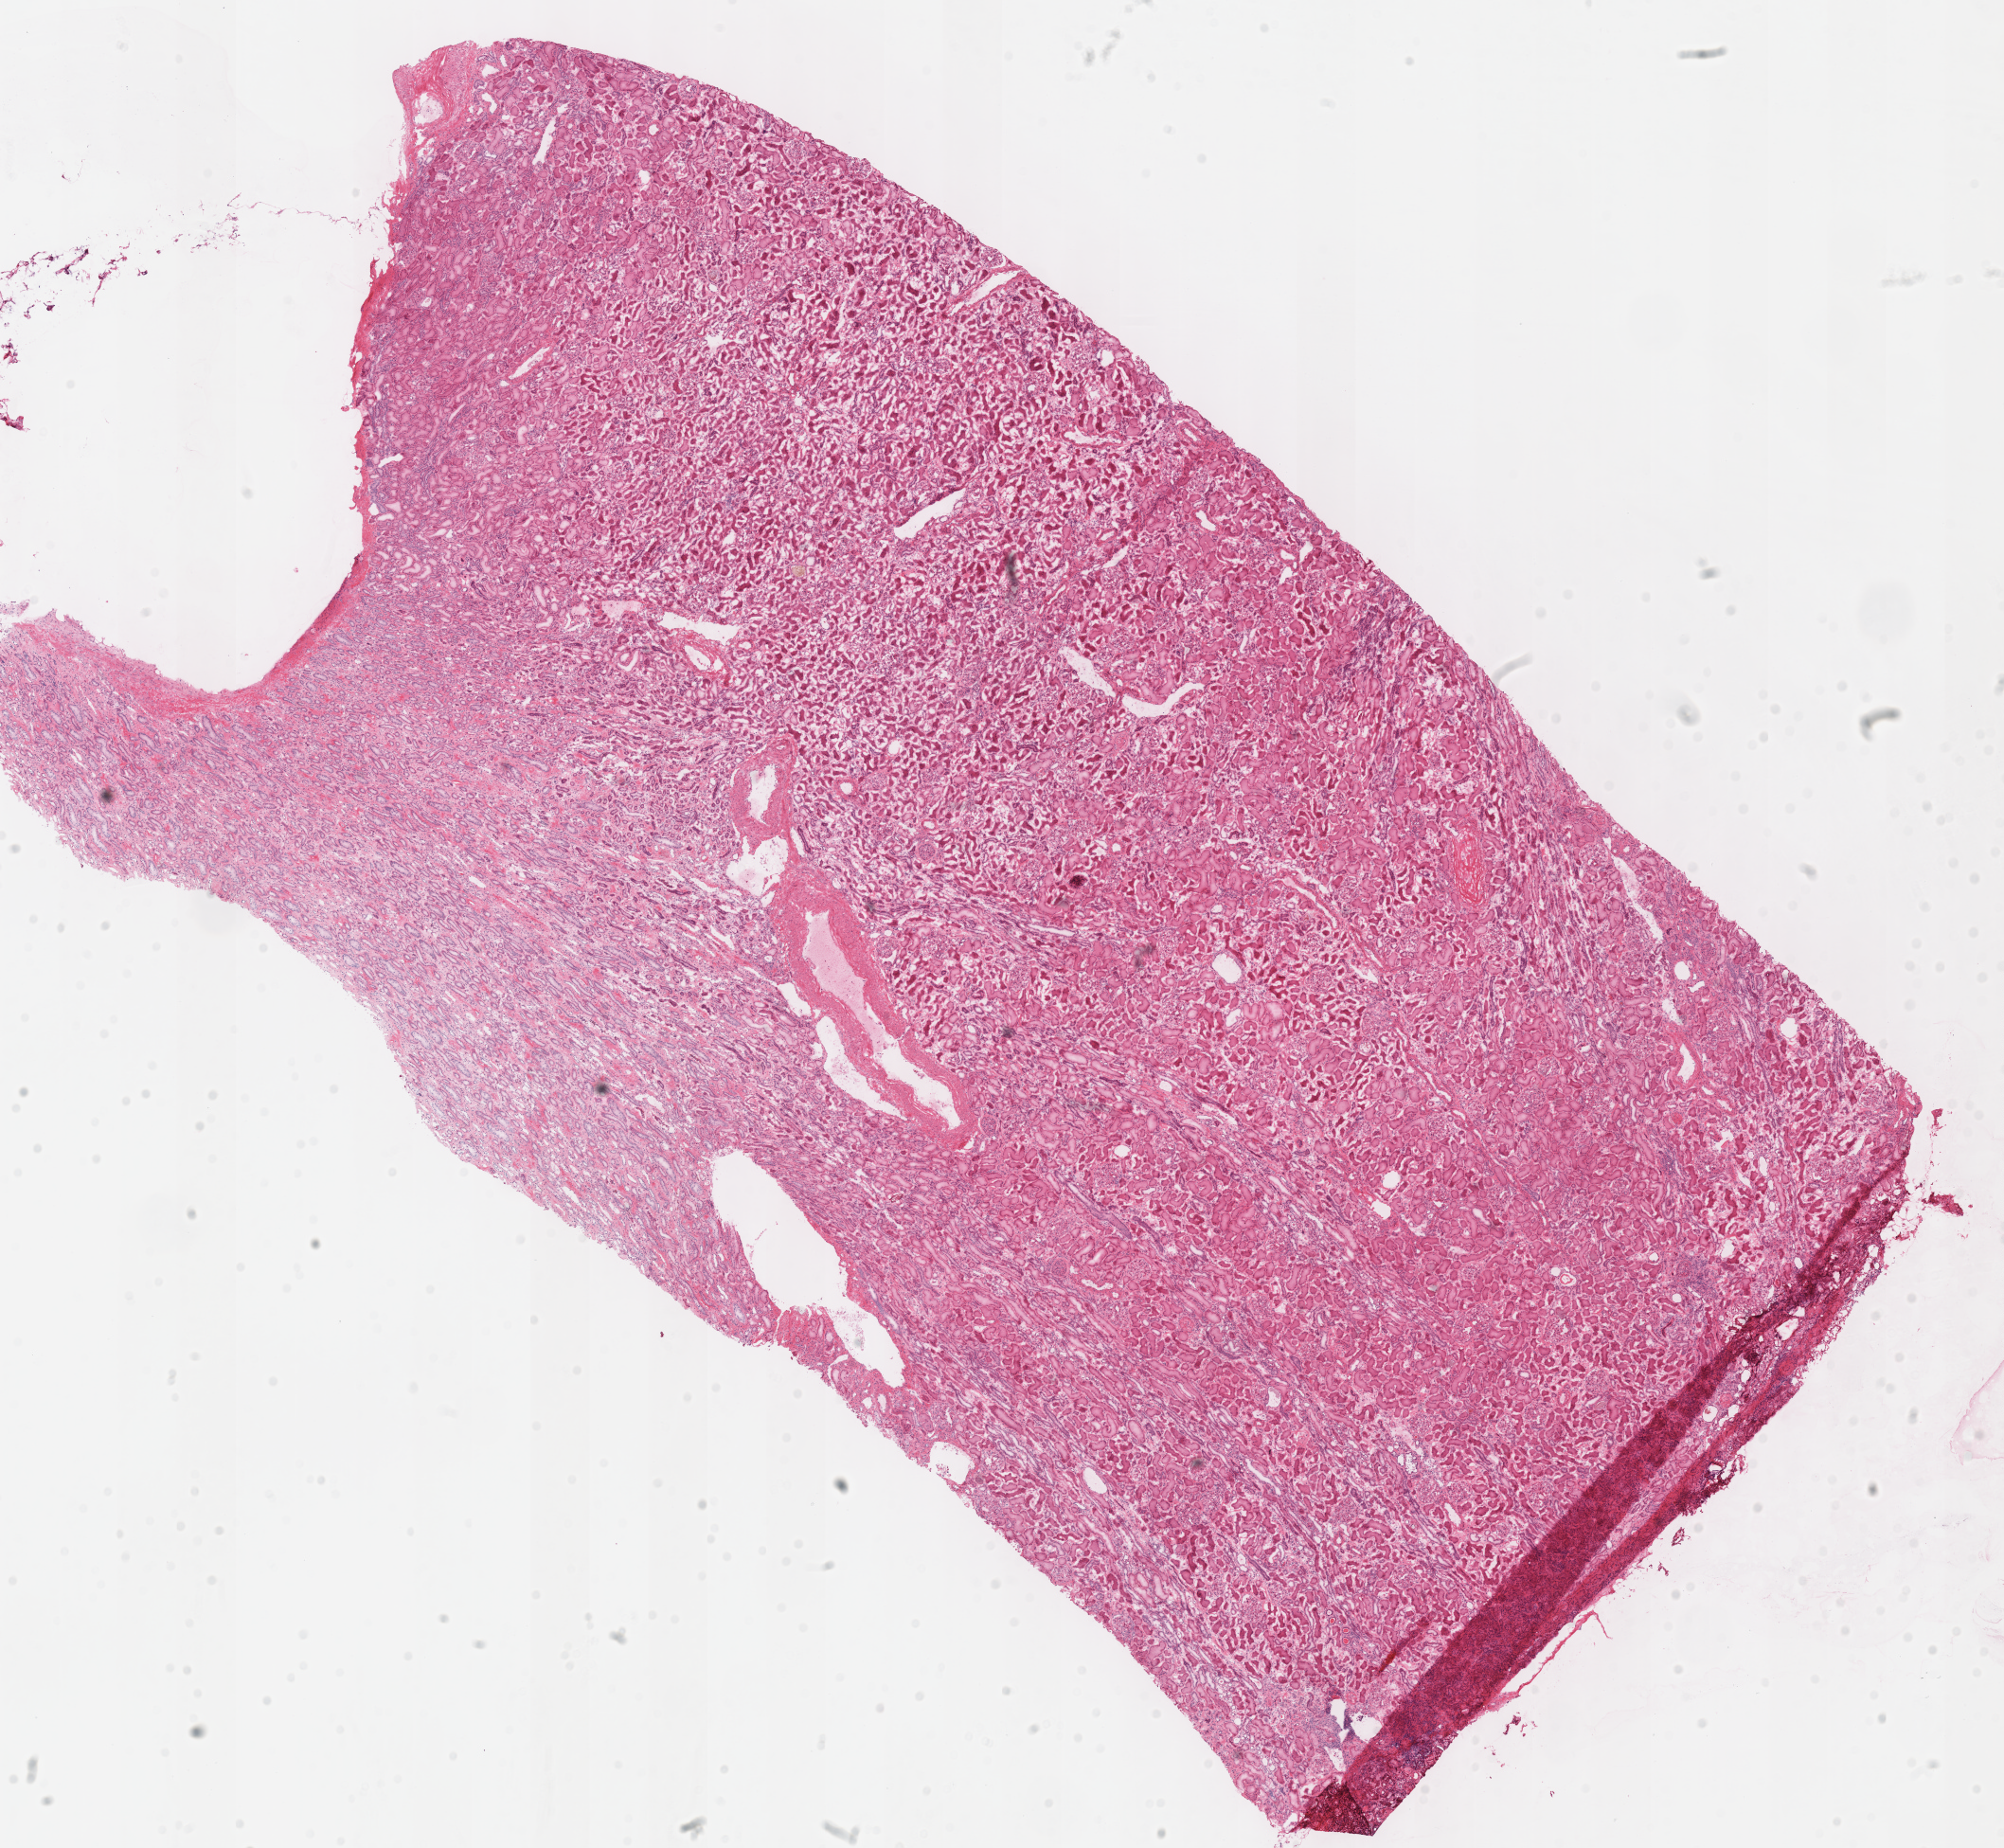
Digitized H&E tissue section (whole slide) — whole scanned area (about 16.6 x 15.3 mm) shown as a low-resolution overview, frozen section from the top of the tissue portion, kidney, solid tissue normal (non-tumour tissue) sample. Patient: male, age at initial diagnosis 75 years.
* this section: solid tissue normal (non-tumour) sample from the same patient
* patient diagnosis: Renal cell carcinoma, chromophobe type